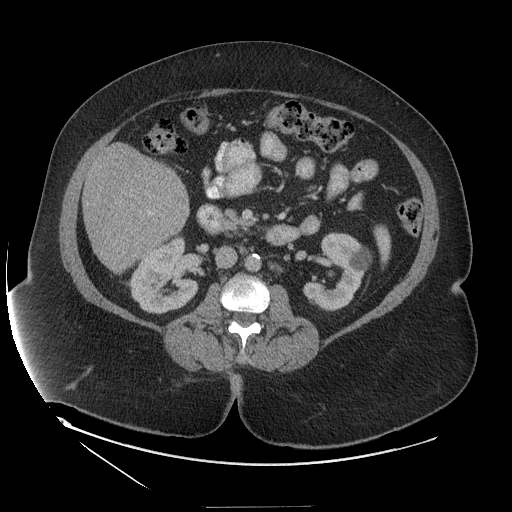
Contrast-enhanced abdominal CT (liver protocol), one axial slice. Slice 46 of 127 in the series (ordered by position). Reconstruction kernel STANDARD. Soft-tissue window (W 400 / L 40 HU). 2.5 mm slice thickness. 512 × 512 image matrix. Case-level facts recorded for this patient, not image findings: diagnosis: hepatocellular carcinoma (patient treated with transarterial chemoembolisation; whether this scan precedes or follows treatment is not stated here); TNM stage (as recorded): Stage-II; Child-Pugh class: A; tumour differentiation: well differentiated; tumour size: 3 cm.
Annotated regions visible in this slice (semi-automatic segmentation, software-assisted and operator-edited):
- liver parenchyma outside the tumour (the mass and vessels are separate outlines, so this box may not span the whole liver): bounding box (x1, y1, x2, y2) in pixels: (82, 144, 188, 272)